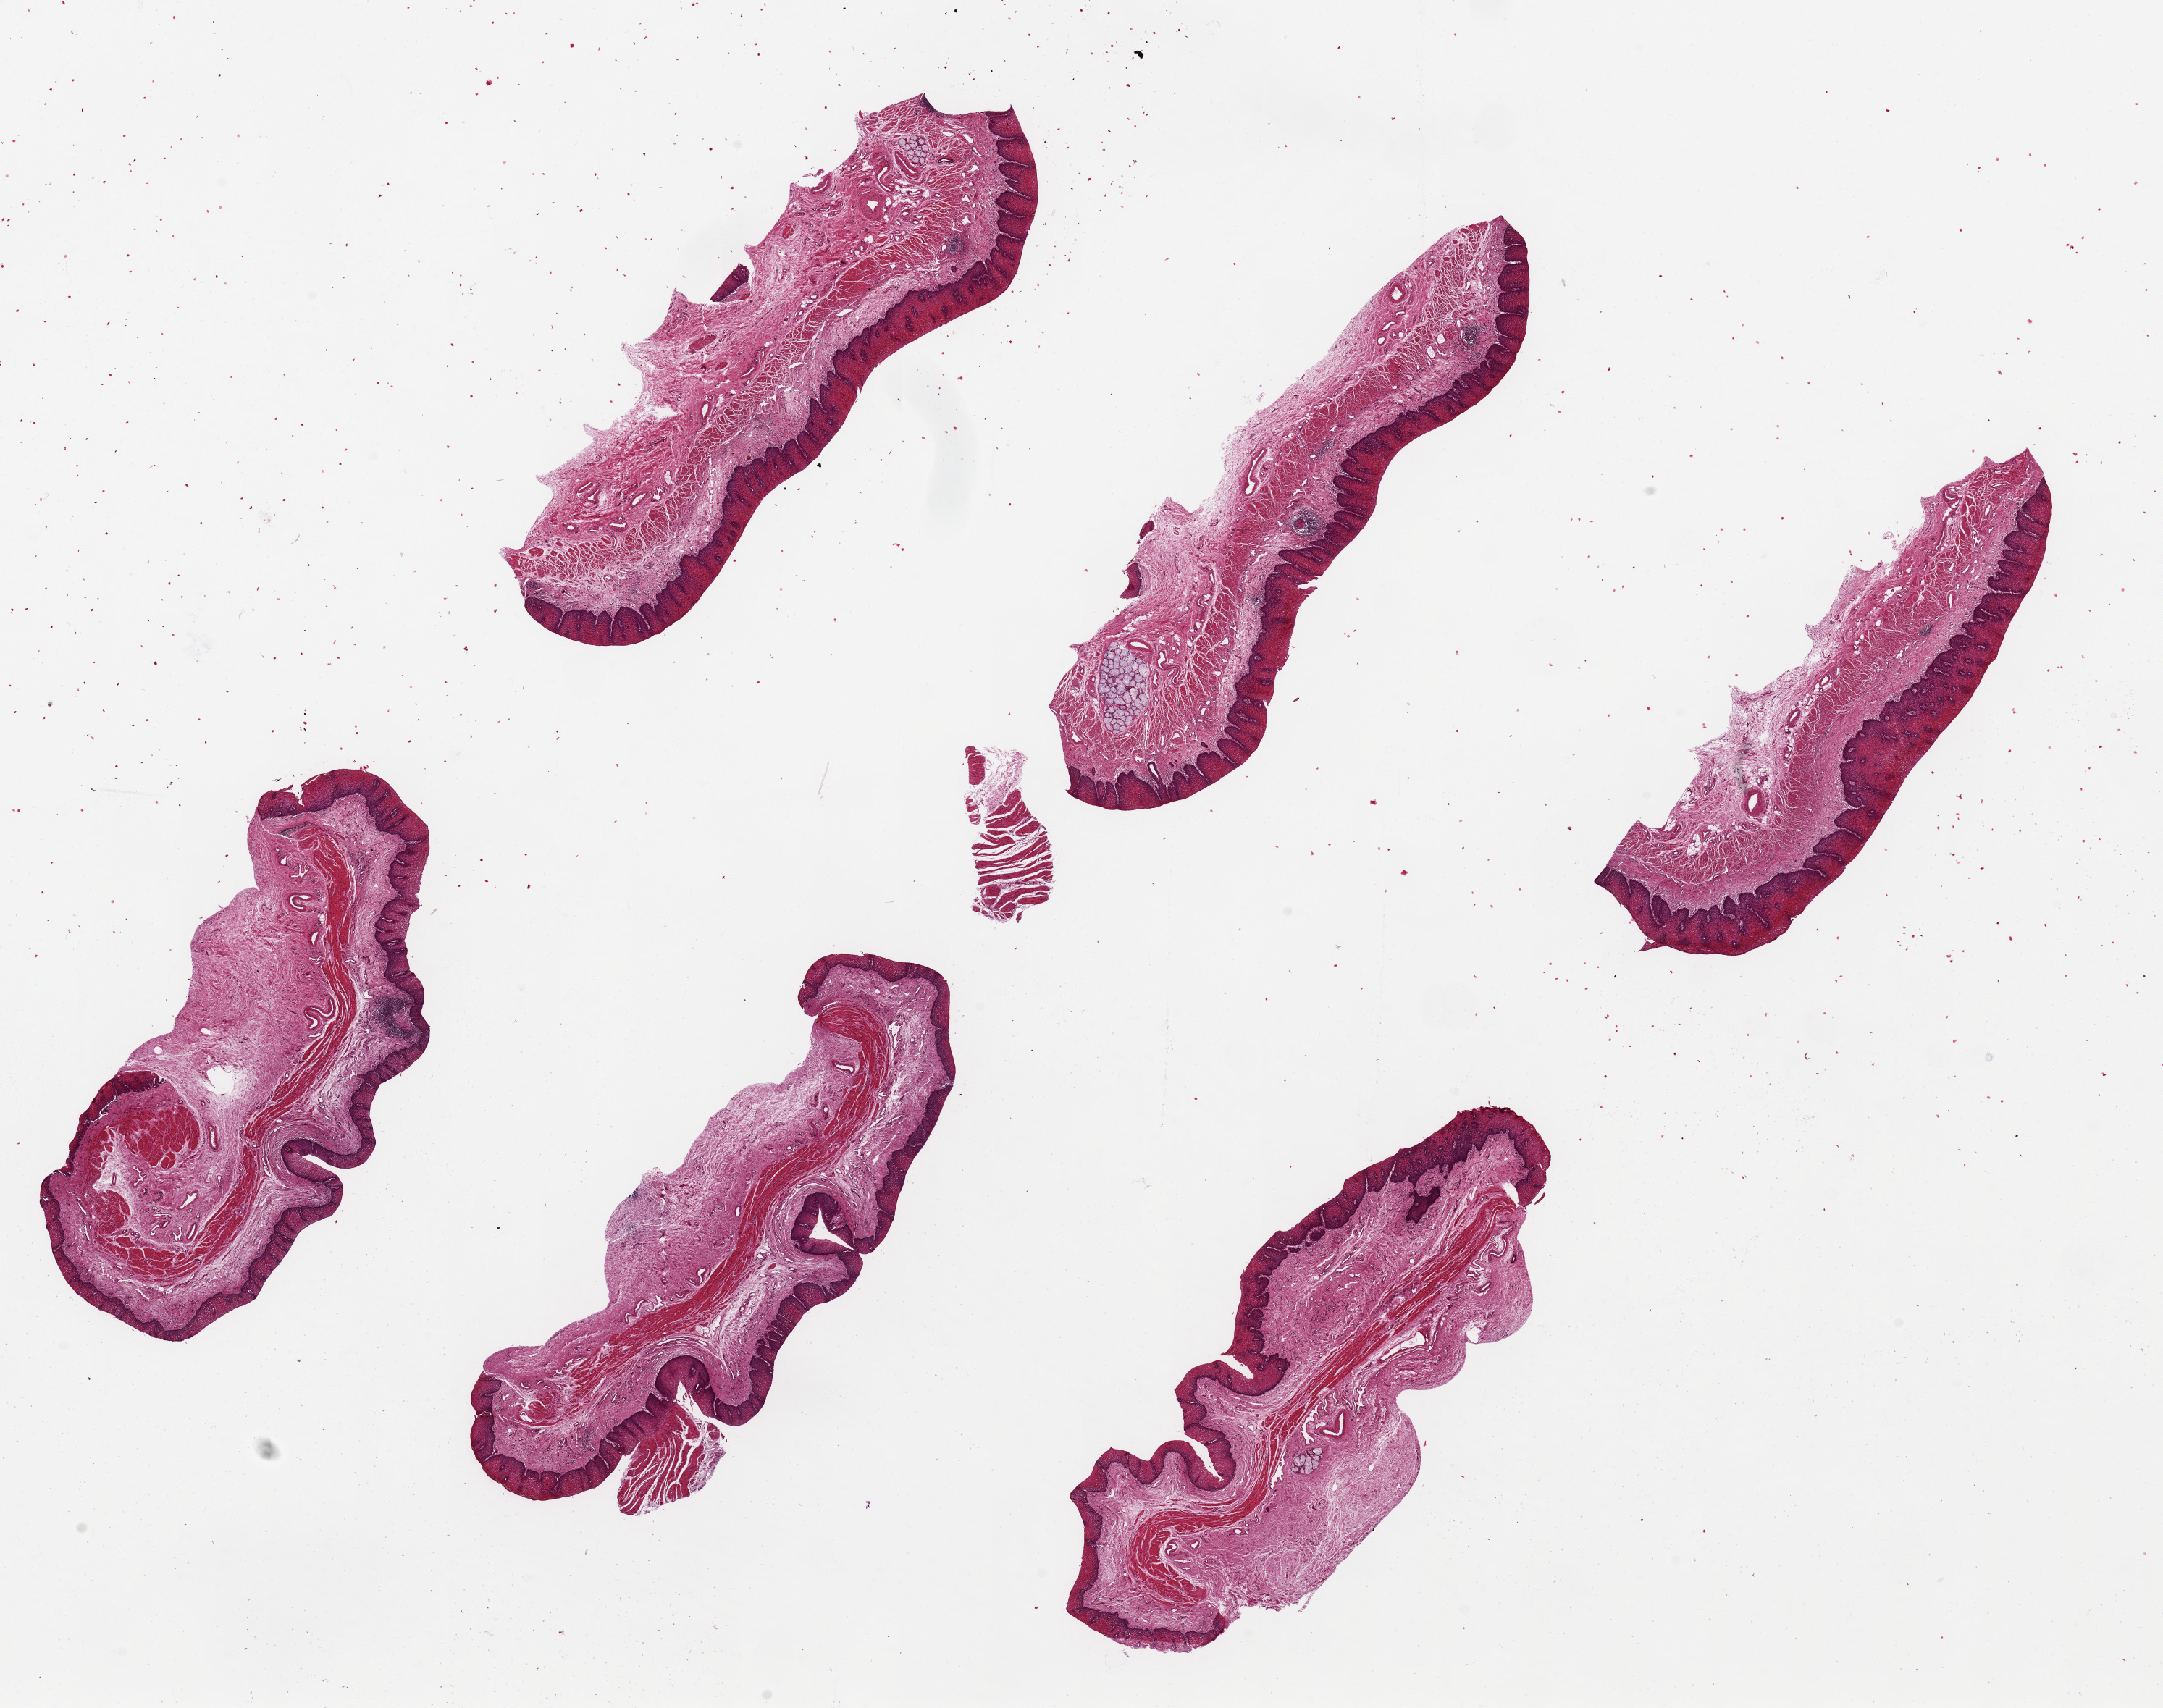
Hematoxylin and eosin (H&E) whole-slide image — a low-resolution overview of the entire scanned area, about 23.6 x 18.7 mm (slide scanned at 20x). PAXgene-fixed paraffin-embedded (PFPE) section. Sampled site (target tissue): esophageal mucous membrane. Tissue donor sample.
Reviewer comment on this tissue sample: 6 pieces, ~7x2mm; Squamous mucosa well preserved, ~15-20% of thickness; Submucosal mucus glands.